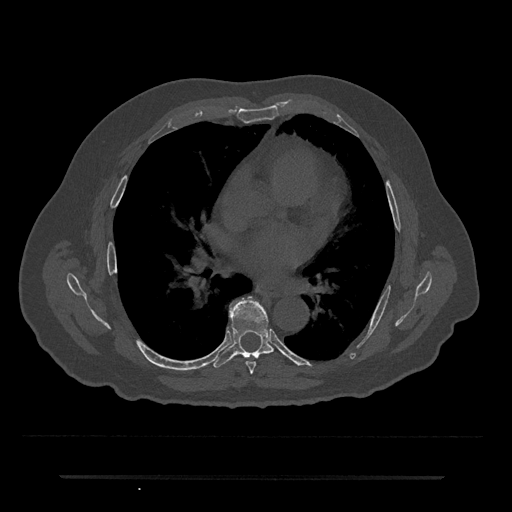
CT including the spine, one axial slice; position 405 of 797 along the scan axis; reconstruction kernel Br40s/3; 120 kVp; bone window (W 1800 / L 400 HU); 512 × 512 image matrix, field of view 437 × 437 mm. Male patient, age 69 years. From the clinical record (not read from this slice): primary cancer: prostate.
Structures marked on this image (semi-automatic segmentation, software-assisted and operator-edited):
- T6 vertebra: box from (x=246, y=362) to (x=256, y=374) px
- T7 vertebra: (x=213, y=297)–(x=274, y=368)